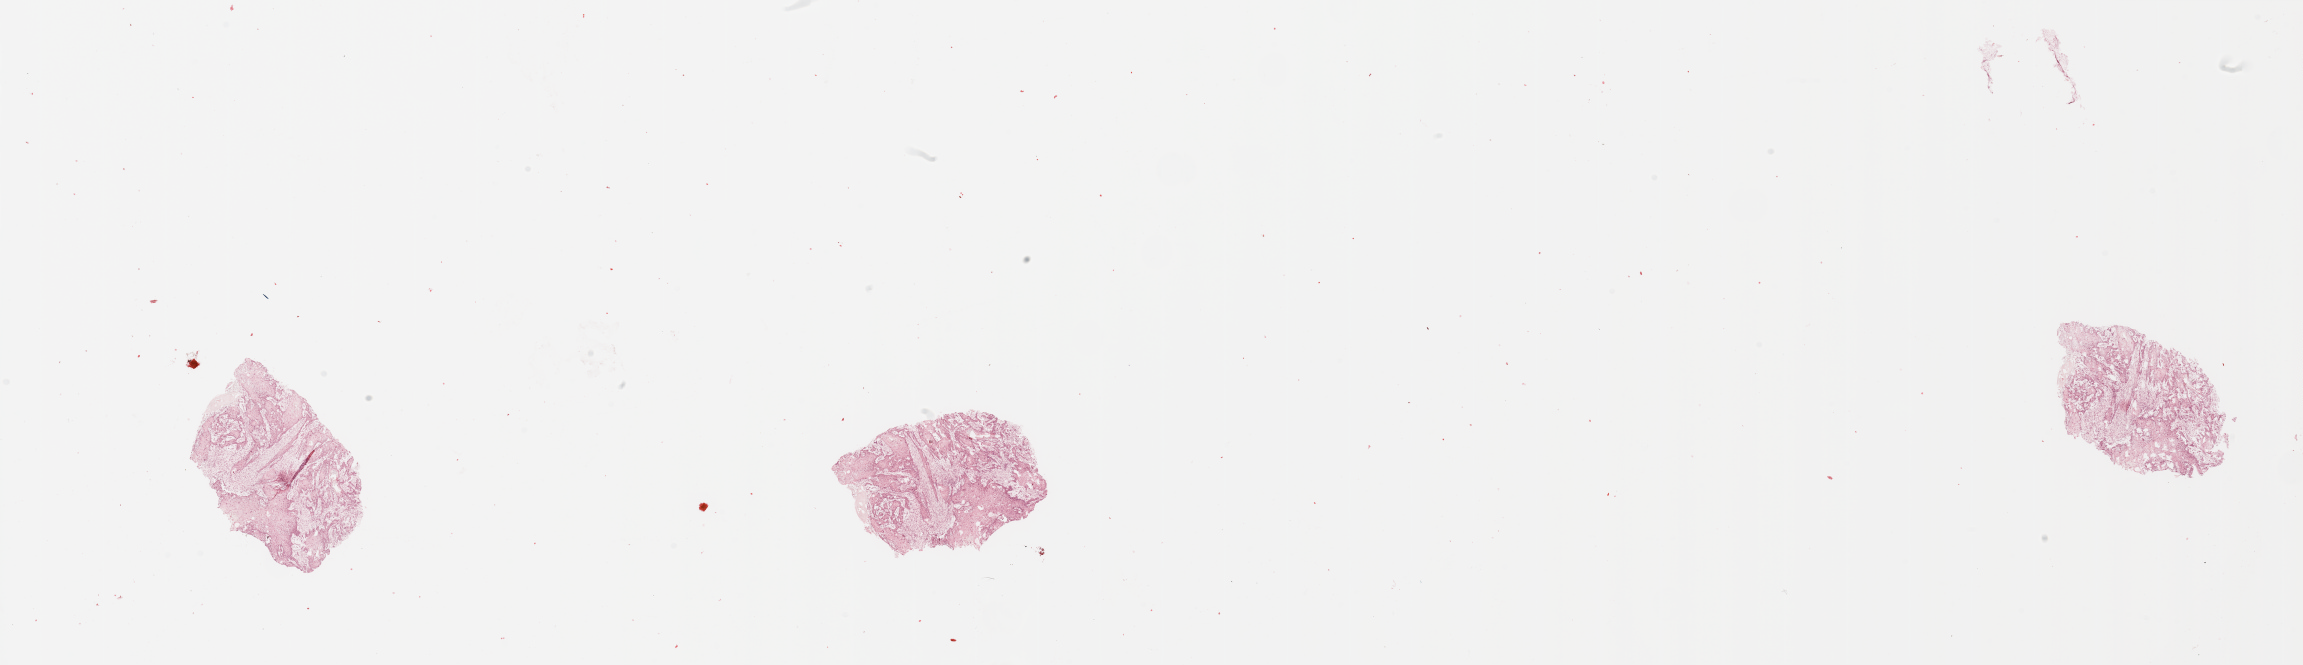
Whole-slide histology image, Hematoxylin and eosin (H&E) stained, a low-resolution overview of the entire scanned area, about 36.4 x 10.5 mm, head and neck, tissue type not recorded. Patient: male, age 73 years.
• patient diagnosis: Squamous cell carcinoma, NOS